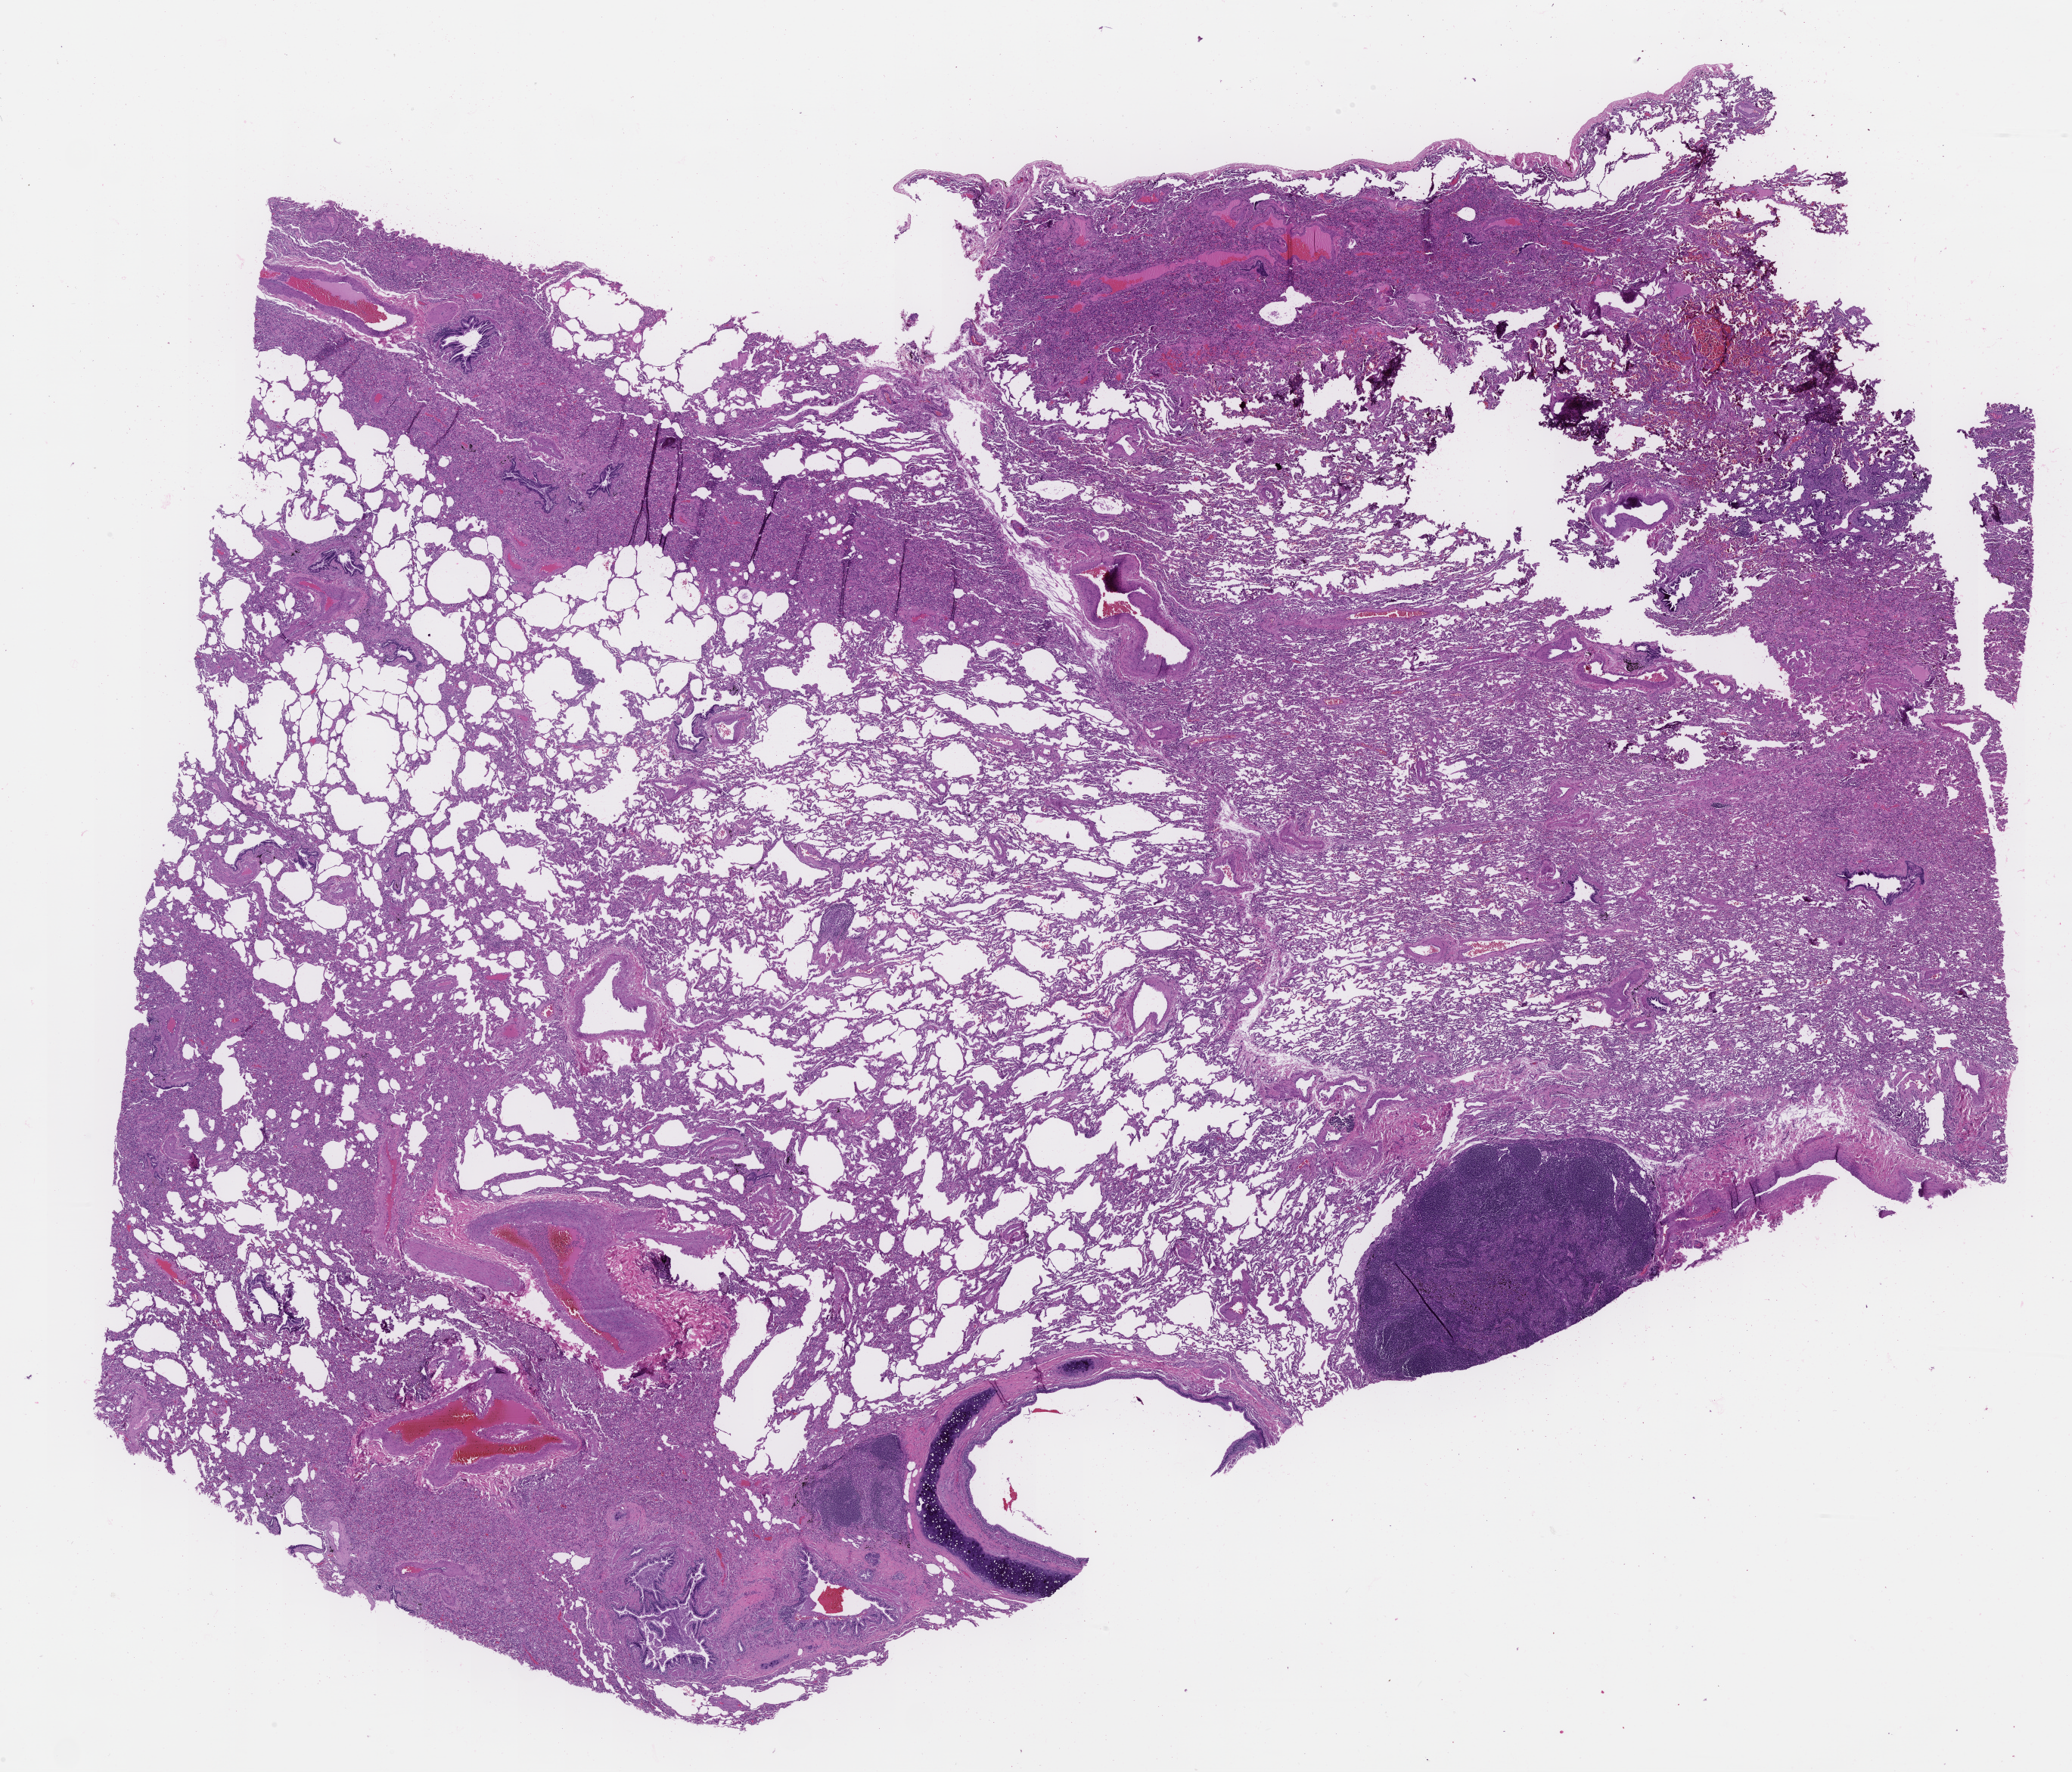
Digitized H&E tissue section (whole slide), shown as a low-resolution overview of the whole scanned area (about 22.1 x 18.9 mm), normal (non-tumour) tissue sample, sampled site: lung. 54-year-old female patient.
This section: normal (non-tumour) tissue from the same patient. Patient diagnosis: Adenocarcinoma, NOS.